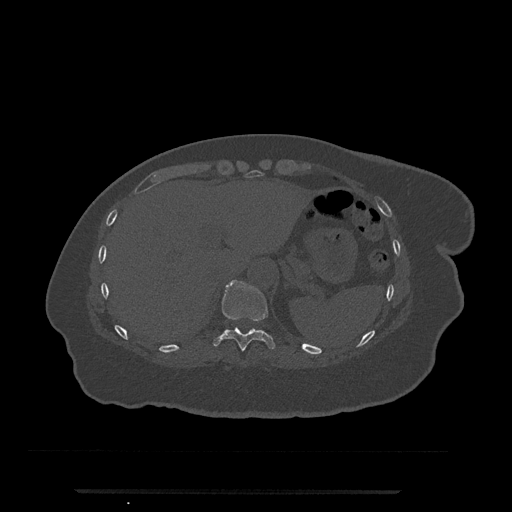
CT including the spine, one axial slice. Slice 279 of 797 in the series (ordered by position). 120 kVp. Bone window (W 1800 / L 400 HU). 0.5 mm slice thickness. 512 × 512 image matrix. Patient: female, 51 years. From the clinical record (not read from this slice): primary cancer: neuro; vertebrae with lytic lesions (as recorded): T8.
Annotated regions visible in this slice (semi-automatic segmentation, software-assisted and operator-edited):
- T10 vertebra: bounding box (x1, y1, x2, y2) in pixels: (212, 280, 275, 351)